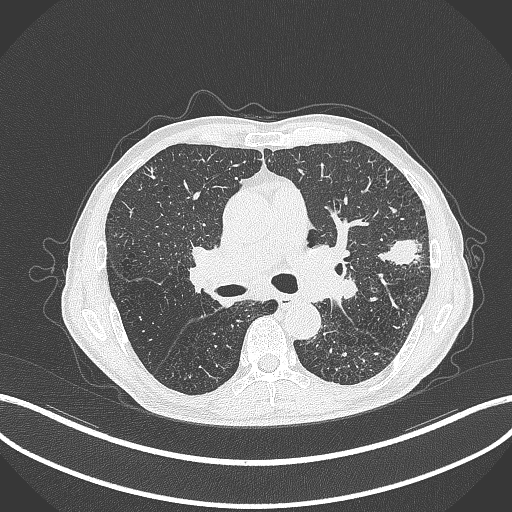
Chest CT, one axial slice; slice 251 of 463 in the series (ordered by position); reconstruction kernel B70f; 120 kVp; lung window (W 1500 / L -600 HU); 1 mm slice thickness; 512 × 512 image matrix, field of view 400 × 400 mm. Patient: male, 74 years. Case-level facts recorded for this patient, not image findings: clinical TNM (as recorded): T2a N1 M0.
Structures marked on this image (bounding box drawn by a radiologist):
- lung tumour (recorded histology: adenocarcinoma): bounding box [x1, y1, x2, y2] px = [374, 233, 430, 268]